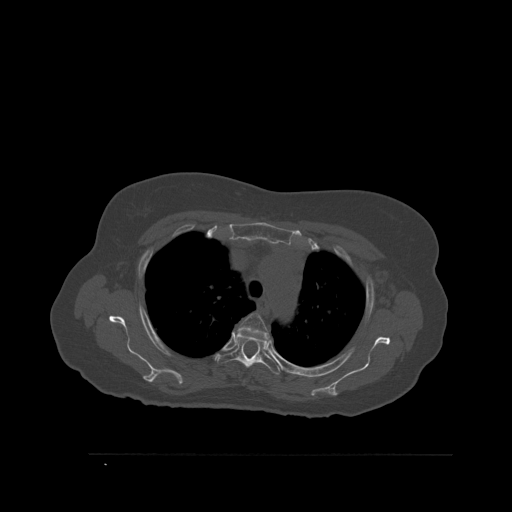
CT including the spine, one axial slice. Position 412 of 527 along the scan axis. Bone window (W 1800 / L 400 HU). 512 × 512 image matrix, field of view 470 × 470 mm. Female patient, age 73 years. Case-level facts recorded for this patient, not image findings: primary cancer: breast; vertebrae with lytic lesions (as recorded): L2.
Annotated regions visible in this slice (semi-automatic segmentation, software-assisted and operator-edited):
- T3 vertebra: box from (x=238, y=313) to (x=270, y=340) px
- T4 vertebra: (x=217, y=331)–(x=280, y=375)